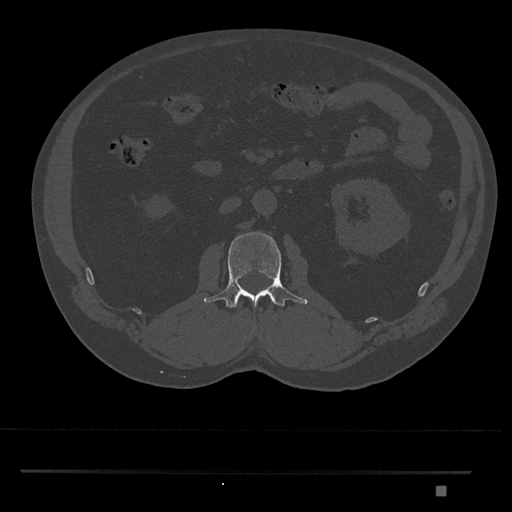
CT including the spine, one axial slice. Slice 758 of 1134 in the series (ordered by position). 120 kVp. Bone window (W 1800 / L 400 HU). 0.5 mm slice thickness. 512 × 512 image matrix, field of view 429 × 429 mm. Male patient, age 65 years. From the clinical record (not read from this slice): primary cancer: prostate.
Structures marked on this image (semi-automatic segmentation, software-assisted and operator-edited):
- L2 vertebra: bounding box (x1, y1, x2, y2) in pixels: (203, 231, 308, 328)